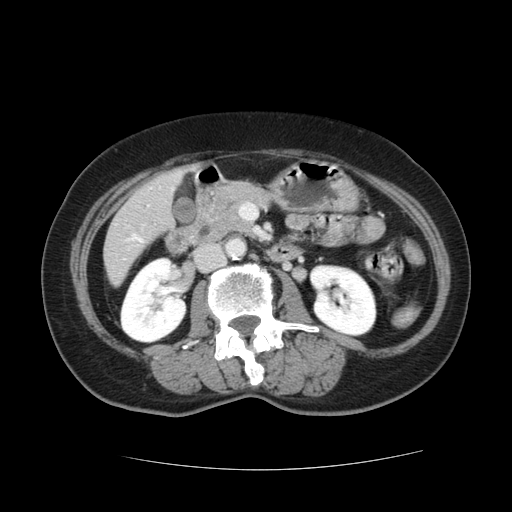
Contrast-enhanced abdominal CT, one axial slice; position 35 of 128 along the scan axis; 120 kVp; intravenous contrast given; soft-tissue window (W 400 / L 40 HU); 2.5 mm slice thickness; 512 × 512 image matrix, field of view 366 × 366 mm. Female patient, age 67 years. Case-level facts recorded for this patient, not image findings: diagnosis: colorectal cancer liver metastases, imaged before liver resection; multiple liver metastases: yes; largest metastasis: 3 cm.
Outlined on this slice (expert manual segmentation):
- liver: bounding box [x1, y1, x2, y2] px = [105, 173, 180, 283]
- planned liver remnant (the part of the liver to remain after resection): [105, 216, 143, 283]